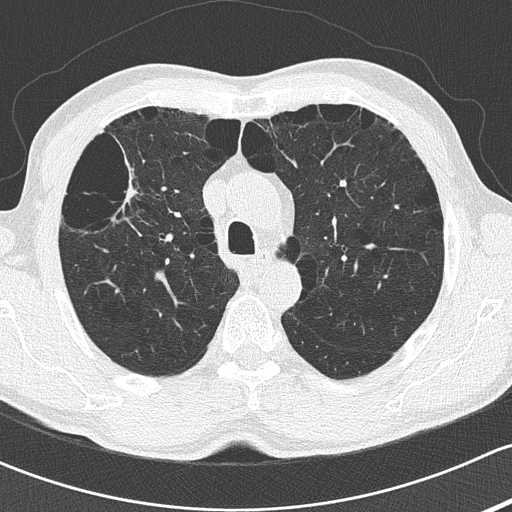
Low-dose screening chest CT, axial slice; second annual screen; lung window (W 1500 / L -600 HU); 2 mm slice thickness; lung (sharp) reconstruction kernel (B50f); slice 46 of 175 in the series; 512 × 512 image matrix, field of view 310 × 310 mm. Male participant, aged 66 years at enrolment. Current smoker at enrolment.
Expert-annotated lung lesion, bounding box (x1, y1, x2, y2) in pixels: (103, 152, 160, 209). The screening reader recorded 3 non-calcified nodules or masses ≥4 mm on this exam (left lower lobe, left lower lobe, left lower lobe); which of them this box marks is not recorded. Official screen result: positive, no significant change: stable abnormalities potentially related to lung cancer, unchanged since the prior screening exam. Lung cancer was diagnosed 566 days after this screen (after the third annual screen): squamous cell carcinoma, adenoid, right upper lobe, poorly differentiated (G3), stage IIB (AJCC 6th edition), 50 mm at pathology.